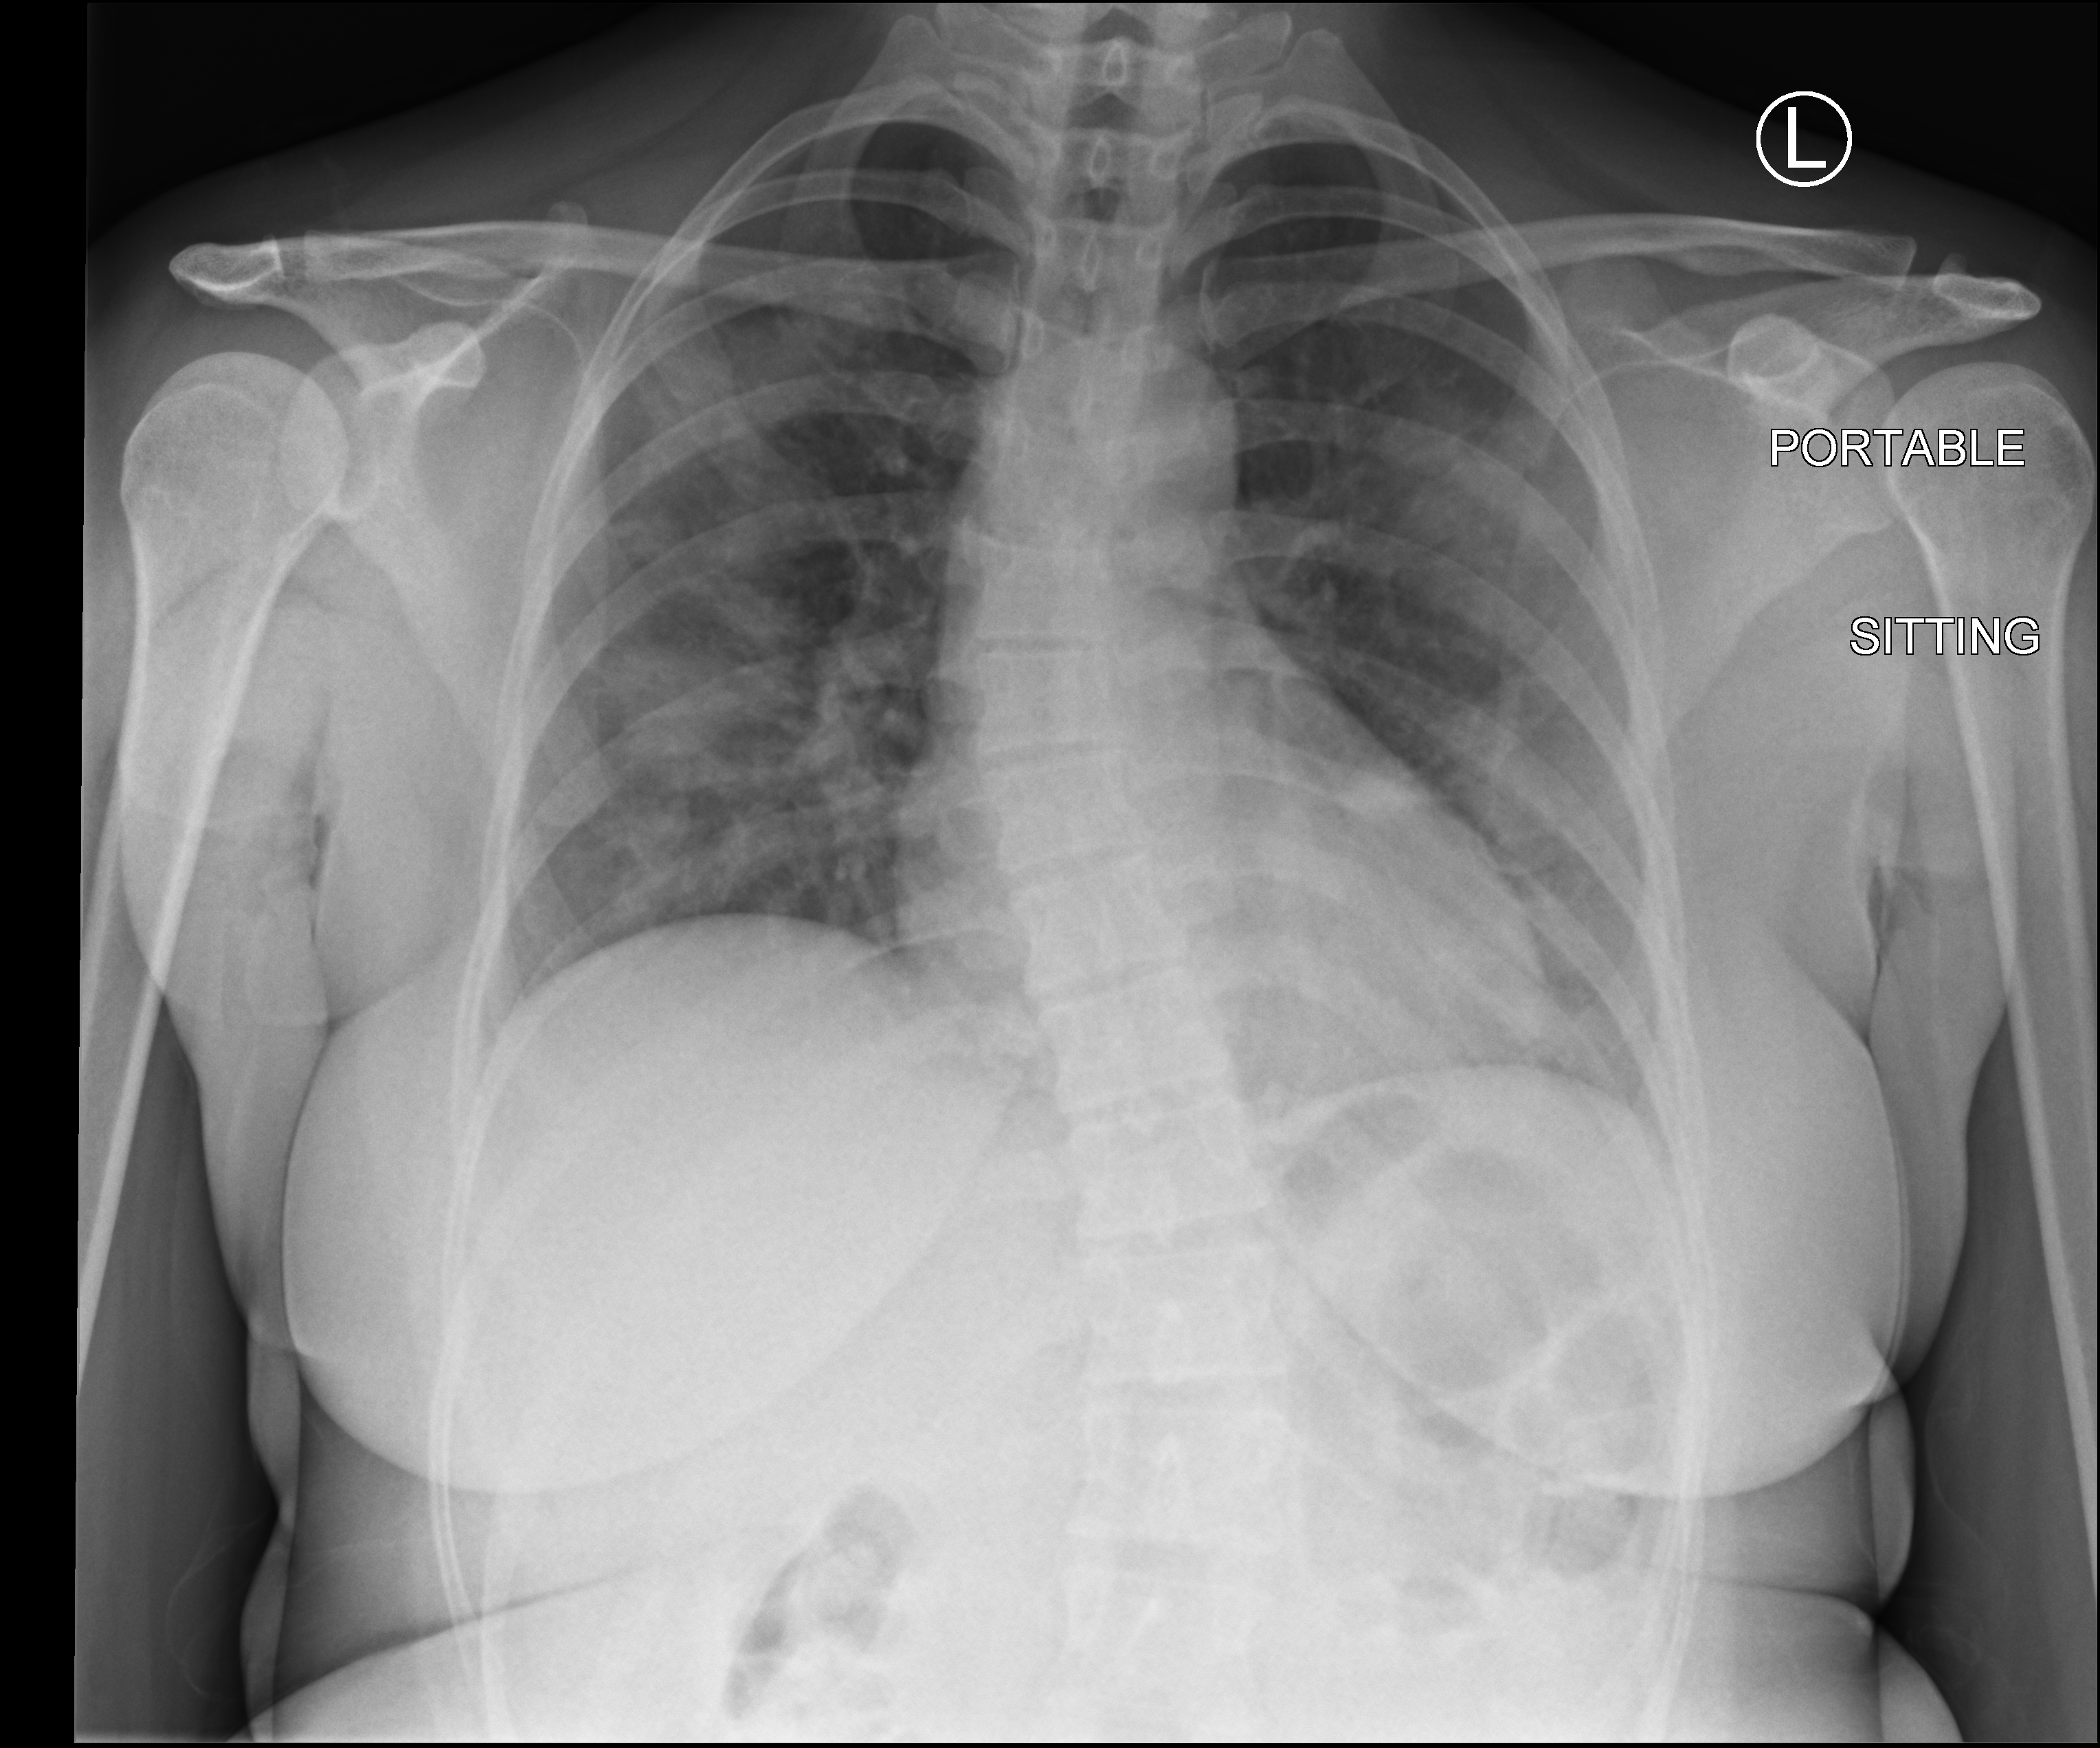
Portable chest radiograph, anteroposterior (AP) projection. Patient hospitalised with COVID-19; female, aged 18–59 years.
From the hospital-stay record, not from the radiograph (when in the stay this image was taken is not recorded): chronic kidney disease (admission record): no; mechanically ventilated during this hospital stay: no.